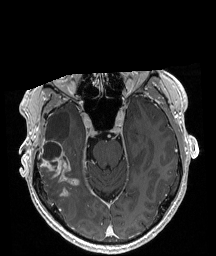
Brain MRI from a brain-tumour surgery series, one axial slice. Position 130 of 208 along the scan axis. T1-weighted post-contrast. 1 mm slice thickness. 216 × 256 image matrix, field of view 211 × 250 mm. From the clinical record (not read from this slice): histopathology: Astrocytoma; WHO grade: 4; IDH mutation: yes; tumour location: Right Temporal.
Structures marked on this image (manually delineated by an expert):
- tumour: box from (x=38, y=141) to (x=78, y=197) px